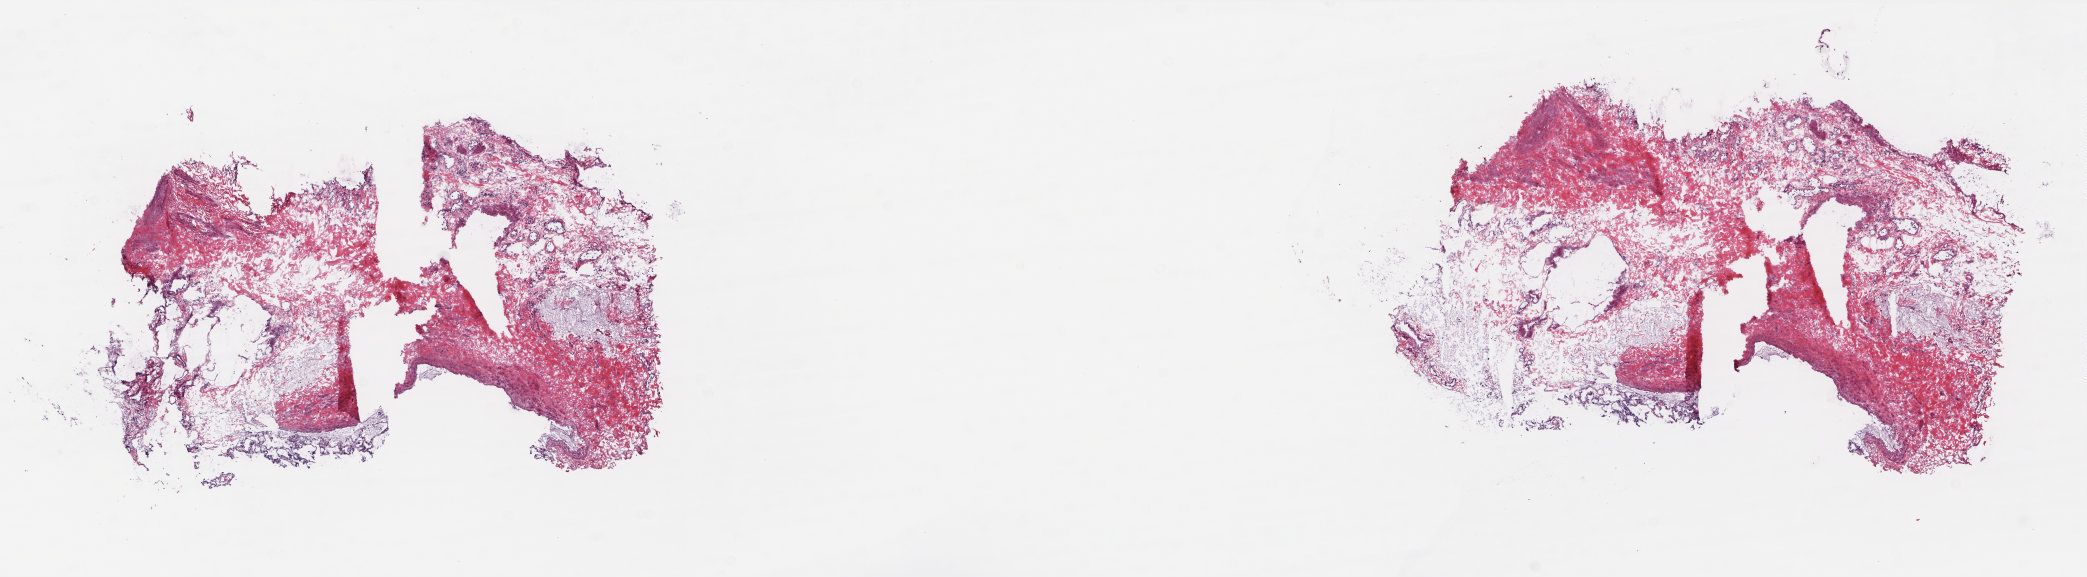
Digitized Hematoxylin and eosin (H&E) stained tissue section (whole slide), low-resolution overview of the scanned area, about 16.8 x 4.7 mm (from a 20x scan); frozen section from the top of the tissue portion; sample: solid tissue normal (non-tumour tissue), lung. Female patient; age at initial diagnosis 60 years. Pathologist review of this section (percent, as recorded): tumour cells 0%, tumour nuclei 0%, normal cells 100%, stromal cells 0%, necrosis 0%. Infiltration values recorded for this section: lymphocyte infiltration 2%, monocyte infiltration 2%, neutrophil infiltration 0%.
* this section: solid tissue normal (non-tumour) sample from the same patient
* patient diagnosis: Adenocarcinoma, NOS (upper lobe, lung)